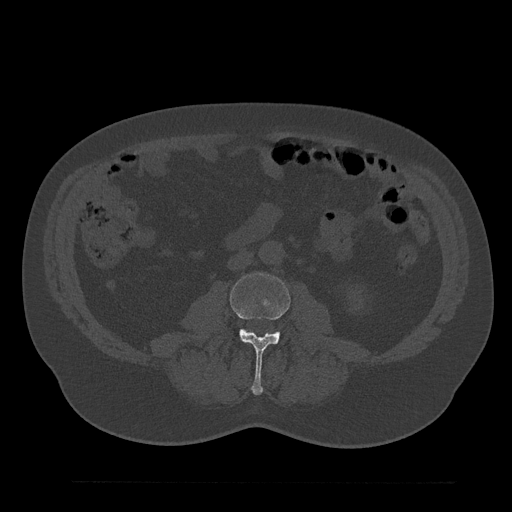
CT including the spine, one axial slice; position 23 of 797 along the scan axis; reconstruction kernel Br40s/3; bone window (W 1800 / L 400 HU); 0.5 mm slice thickness; 512 × 512 image matrix. Male patient, age 61 years. From the clinical record (not read from this slice): primary cancer: prostate.
Annotated regions visible in this slice (semi-automatically segmented with operator editing):
- L3 vertebra: box from (x=230, y=273) to (x=290, y=395) px